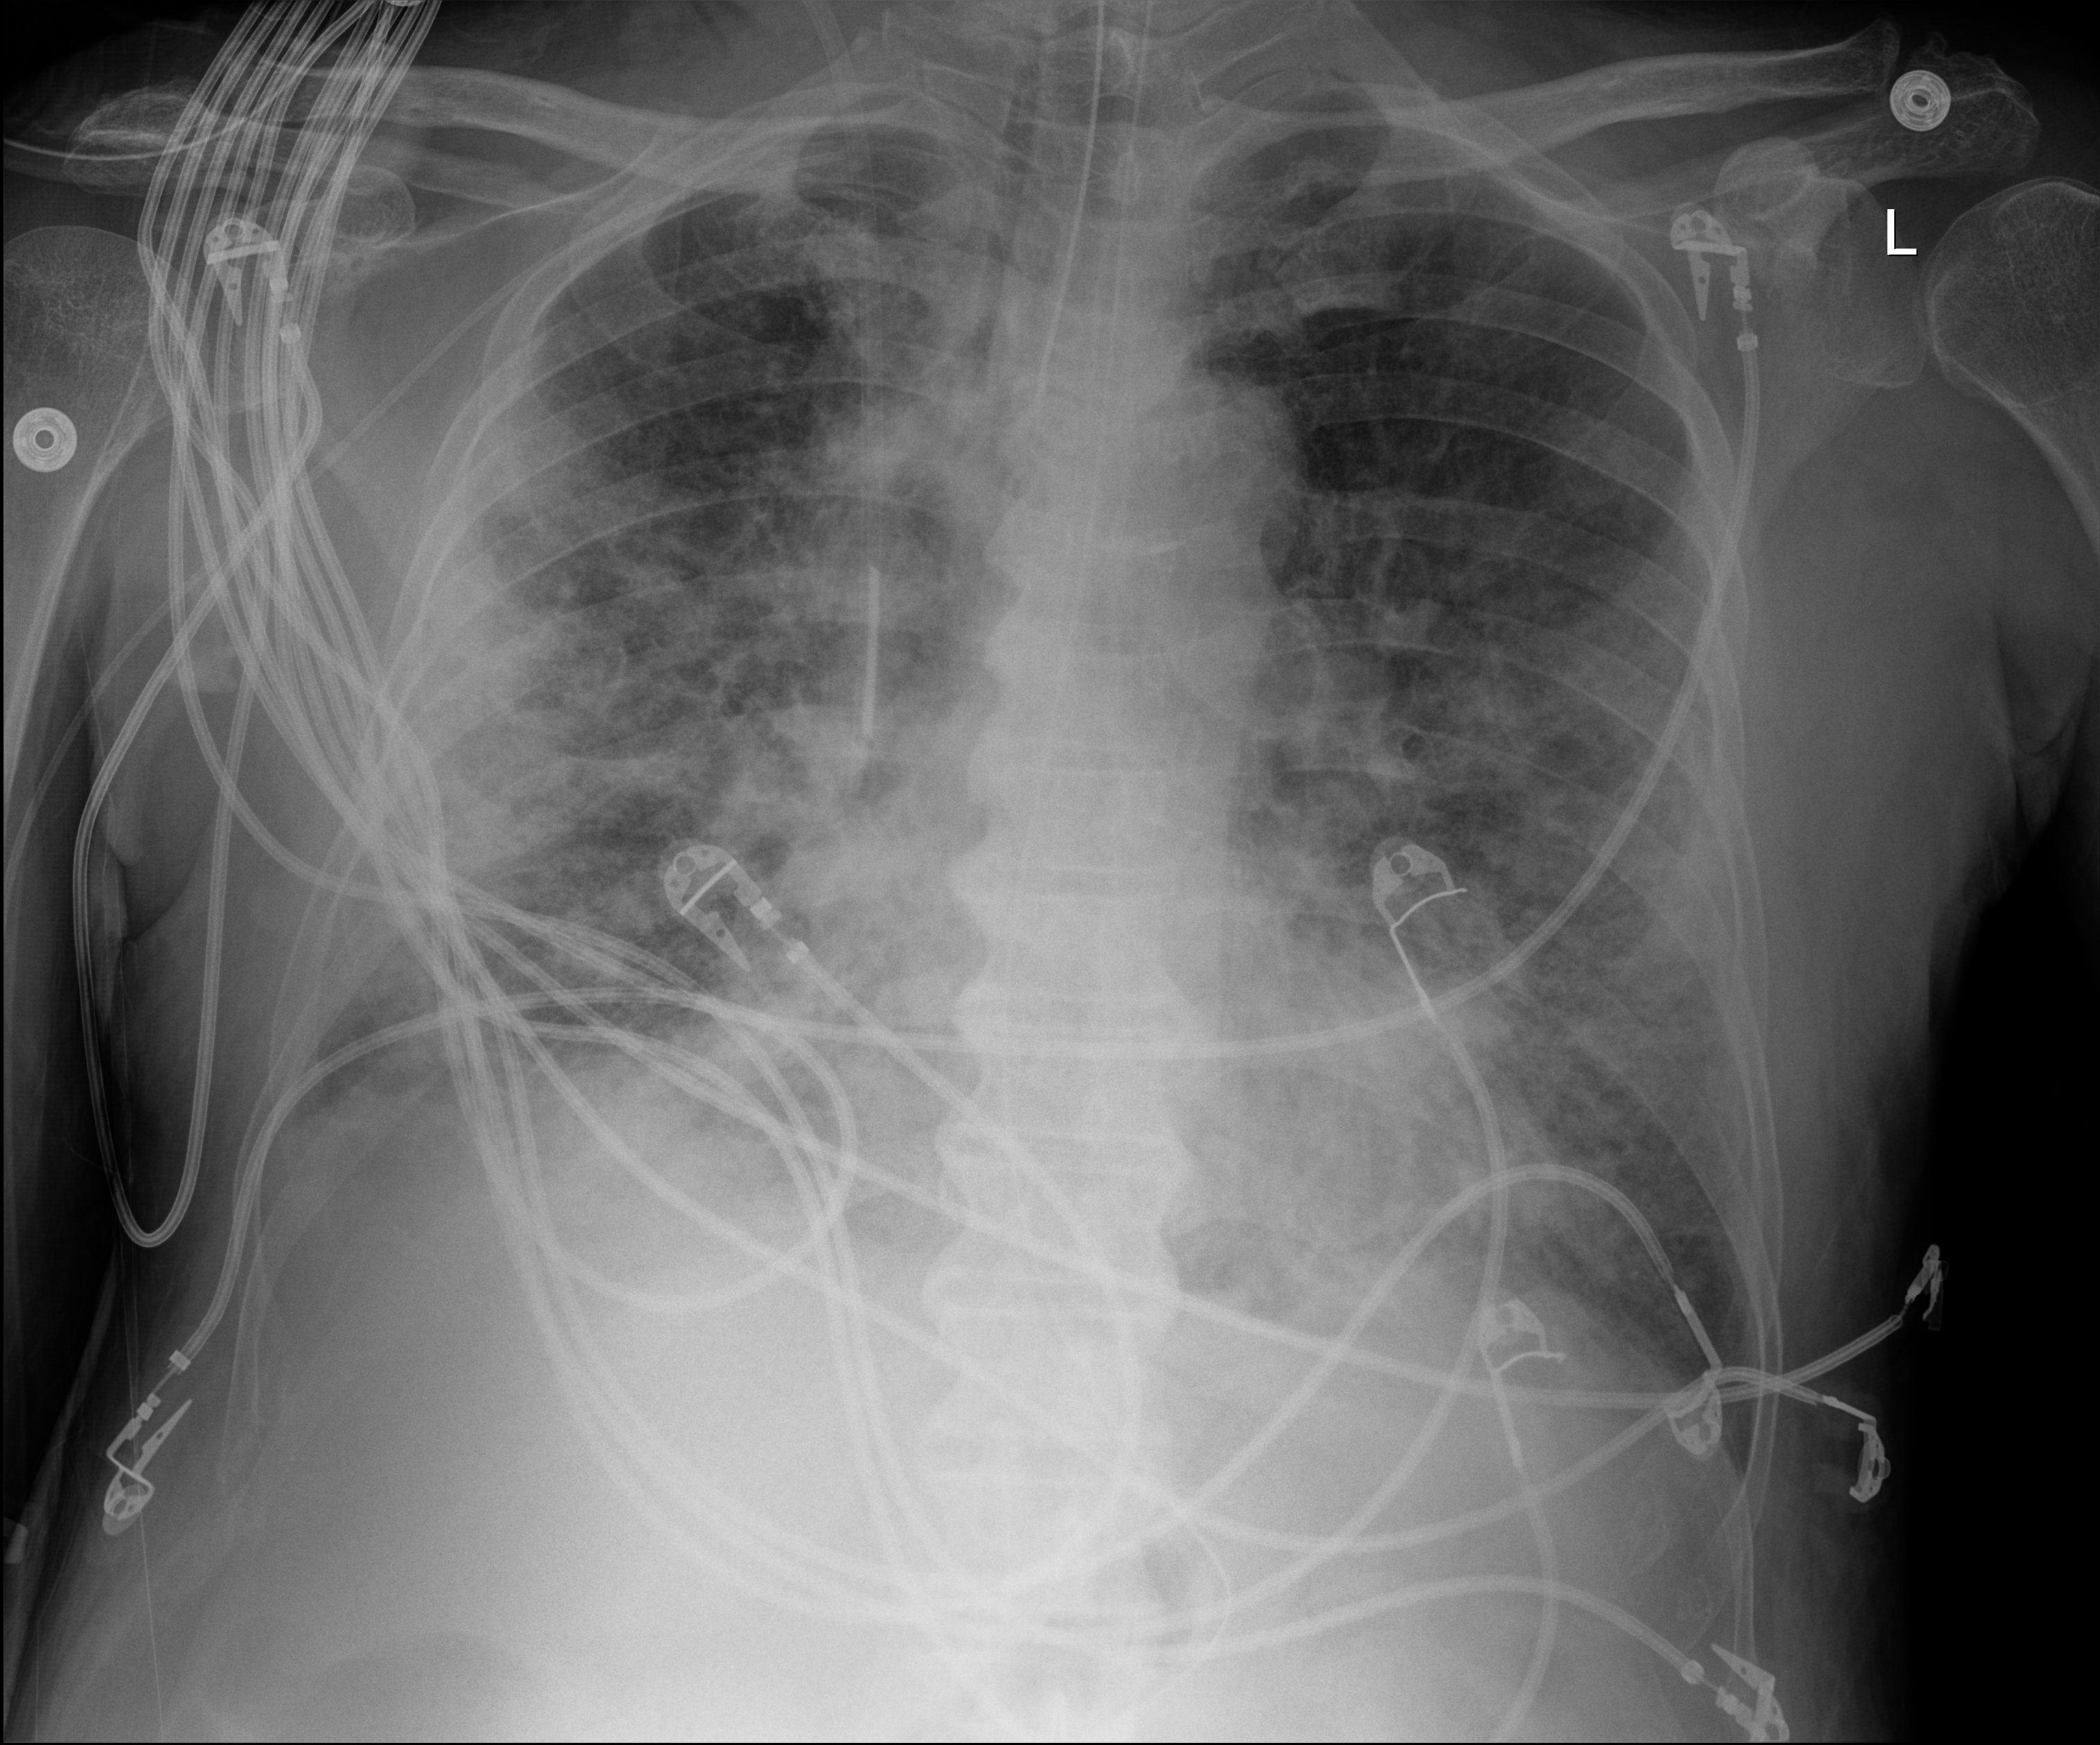
Portable chest radiograph, anteroposterior (AP) projection. Male patient hospitalised with COVID-19, age 60–74 years.
Hospital-stay facts (about this admission, not read from this image; timing relative to this image not recorded): admitted to intensive care during this hospital stay: yes.